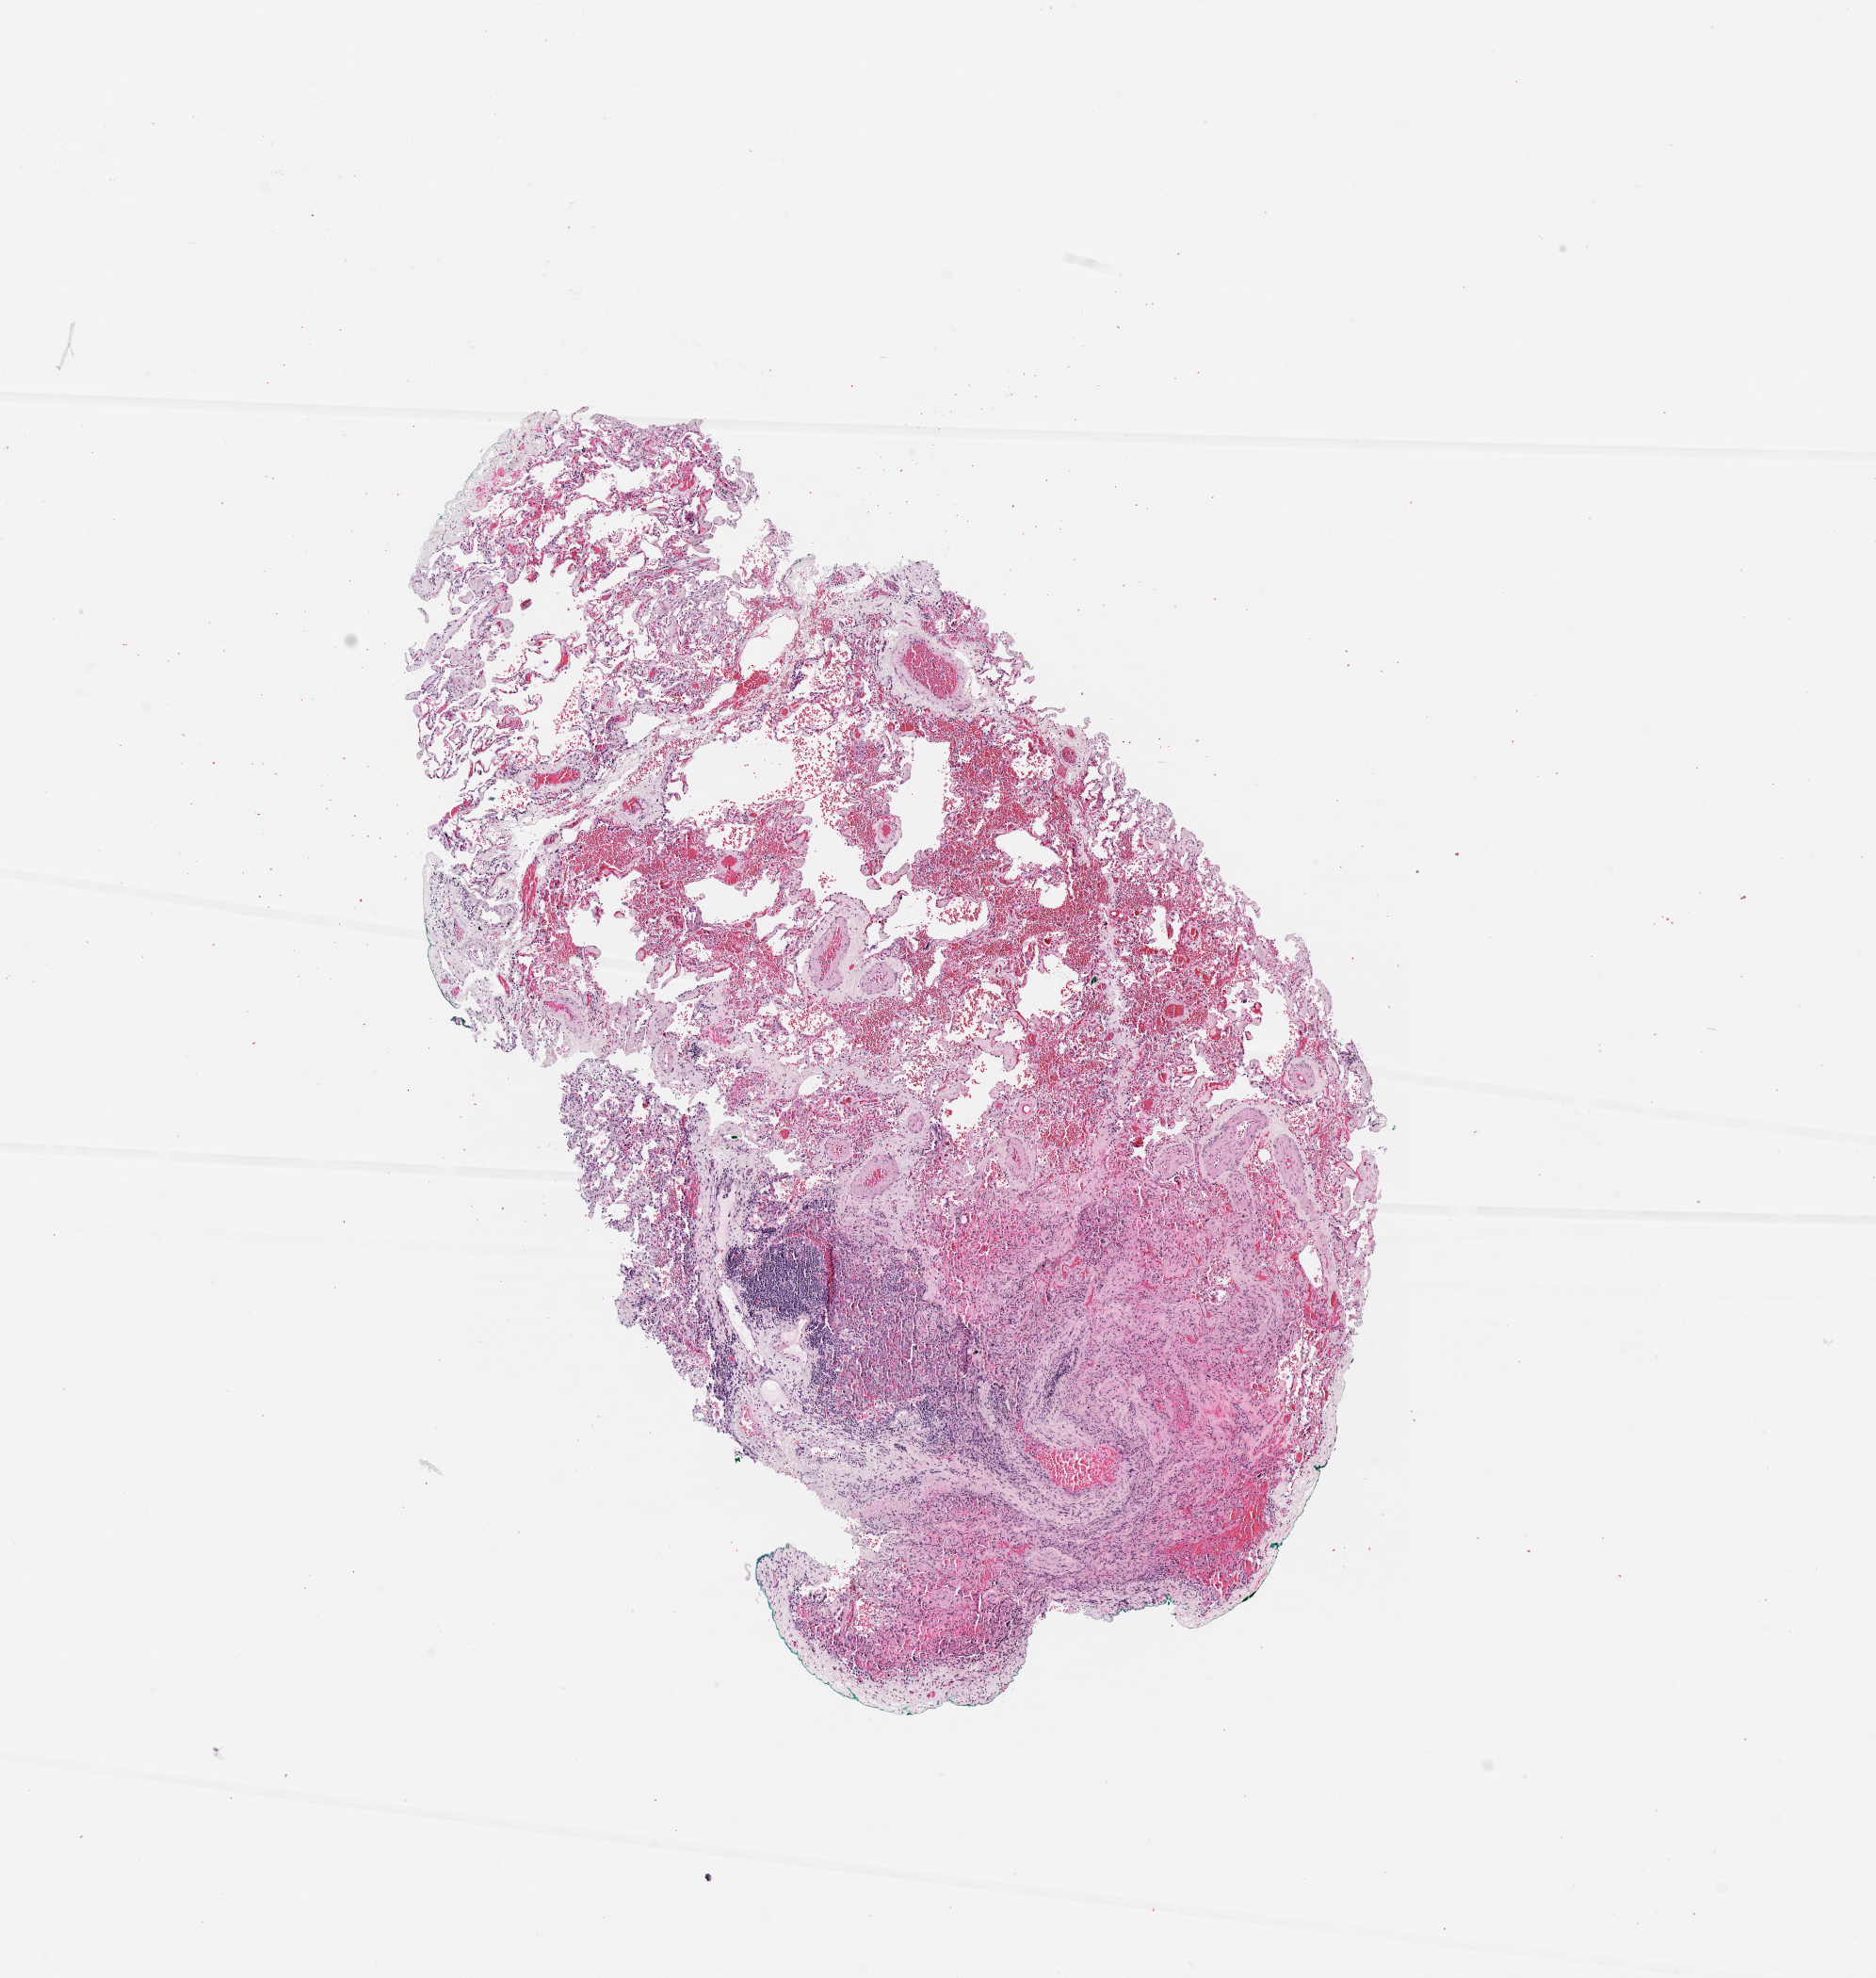
Whole-slide histology image, Hematoxylin and eosin (H&E) stained, shown as a low-resolution overview of the whole scanned area (about 8.0 x 8.5 mm), lung, normal (non-tumour) tissue. Patient: female, age 71 years.
This section: normal (non-tumour) tissue from the same patient. Patient diagnosis (cohort enrolment): squamous cell carcinoma (lung).